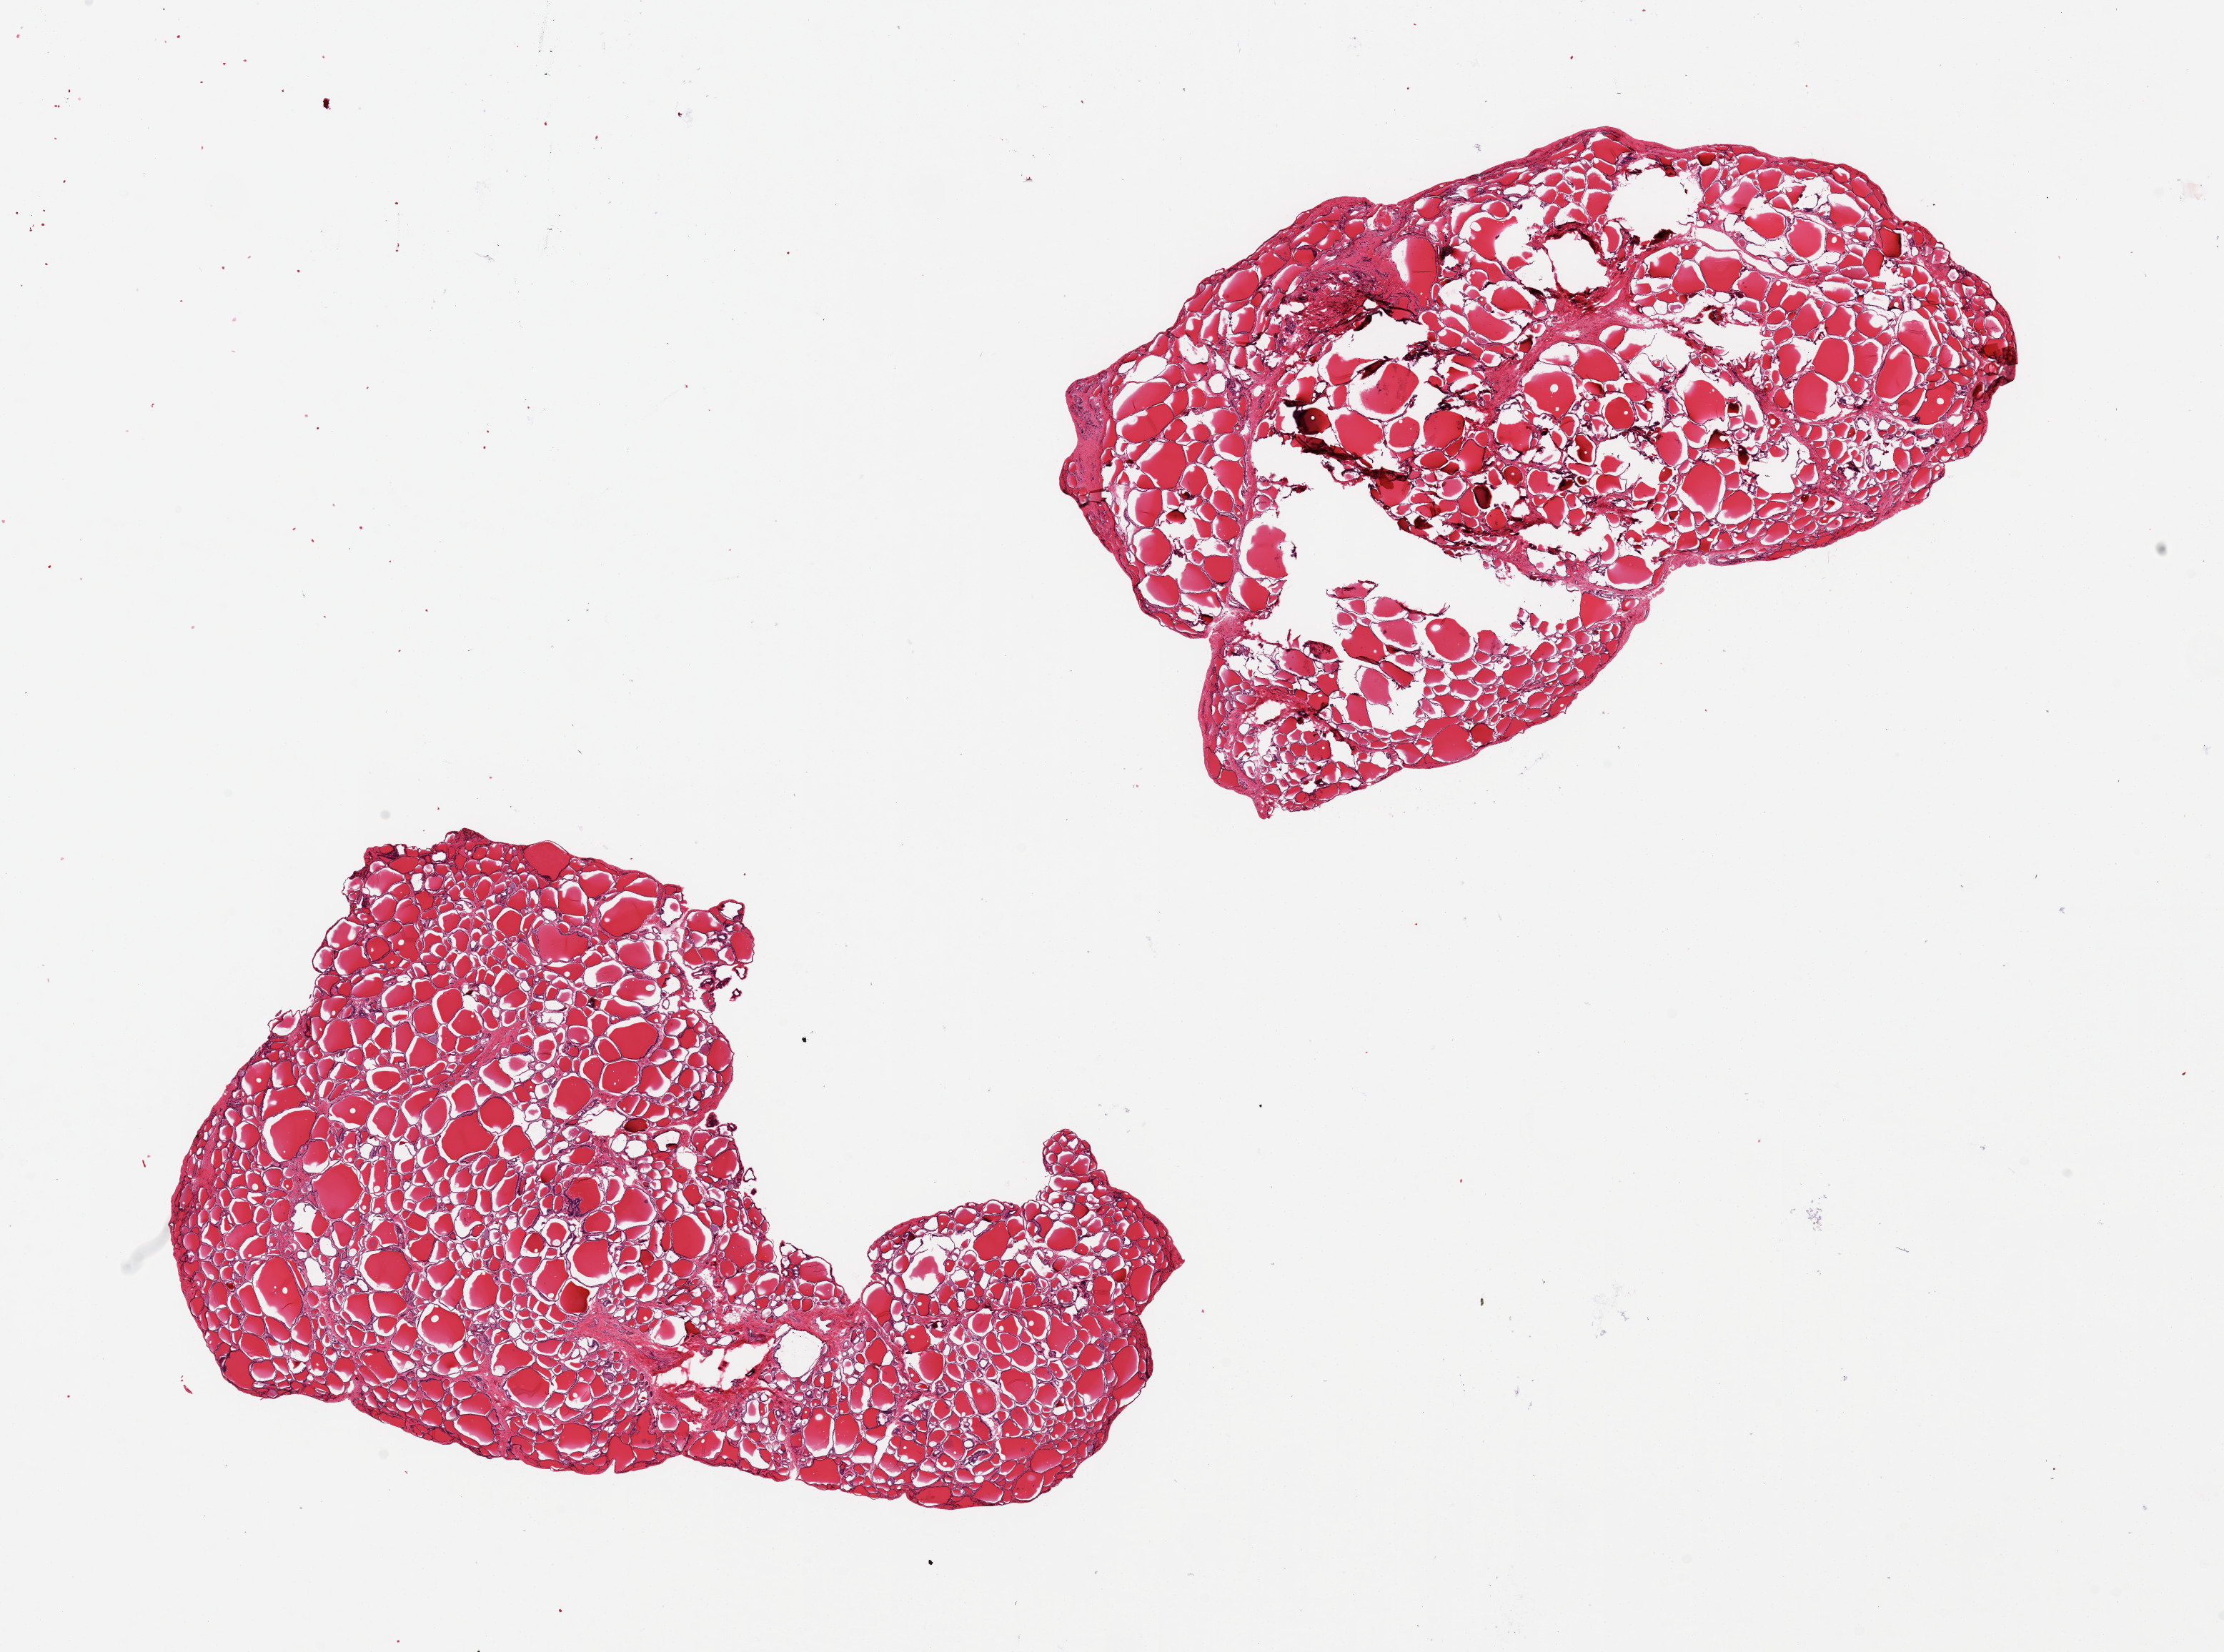
Whole-slide image, hematoxylin and eosin (H&E) stain, shown as a low-resolution overview of the whole scanned area (about 24.6 x 18.3 mm, slide scanned at 20x). PAXgene-fixed, paraffin-embedded tissue. Section of thyroid (target tissue). Donor tissue sample.
* review note (as recorded): 2 pieces, 10x6 & 11x7mm; No extraneous tissue